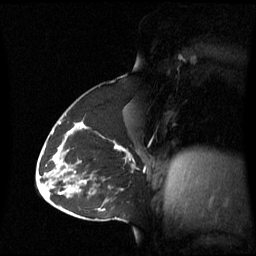
Breast MRI (dynamic contrast-enhanced), one sagittal slice. Slice 35 of 60 in the series (ordered by position). Dynamic contrast-enhanced series, image 2 of 3 at this slice position (ordered by acquisition). 1.5 T. TE 4.2 ms, TR 8.4 ms. 2.8 mm slice thickness. 256 × 256 image matrix. Patient: female, 43 years. From the clinical record (not read from this slice): setting: breast cancer imaged before/during neoadjuvant chemotherapy; receptor status: triple-negative.
Annotated regions visible in this slice (semi-automatically segmented with operator editing):
- analysis volume of interest (the breast-tissue region the enhancement analysis was run in; not a lesion): bounding box [x1, y1, x2, y2] px = [62, 124, 135, 180]
- tumour enhancement mask (voxels above the 70 % enhancement threshold inside the analysis volume of interest): [81, 124, 134, 162]